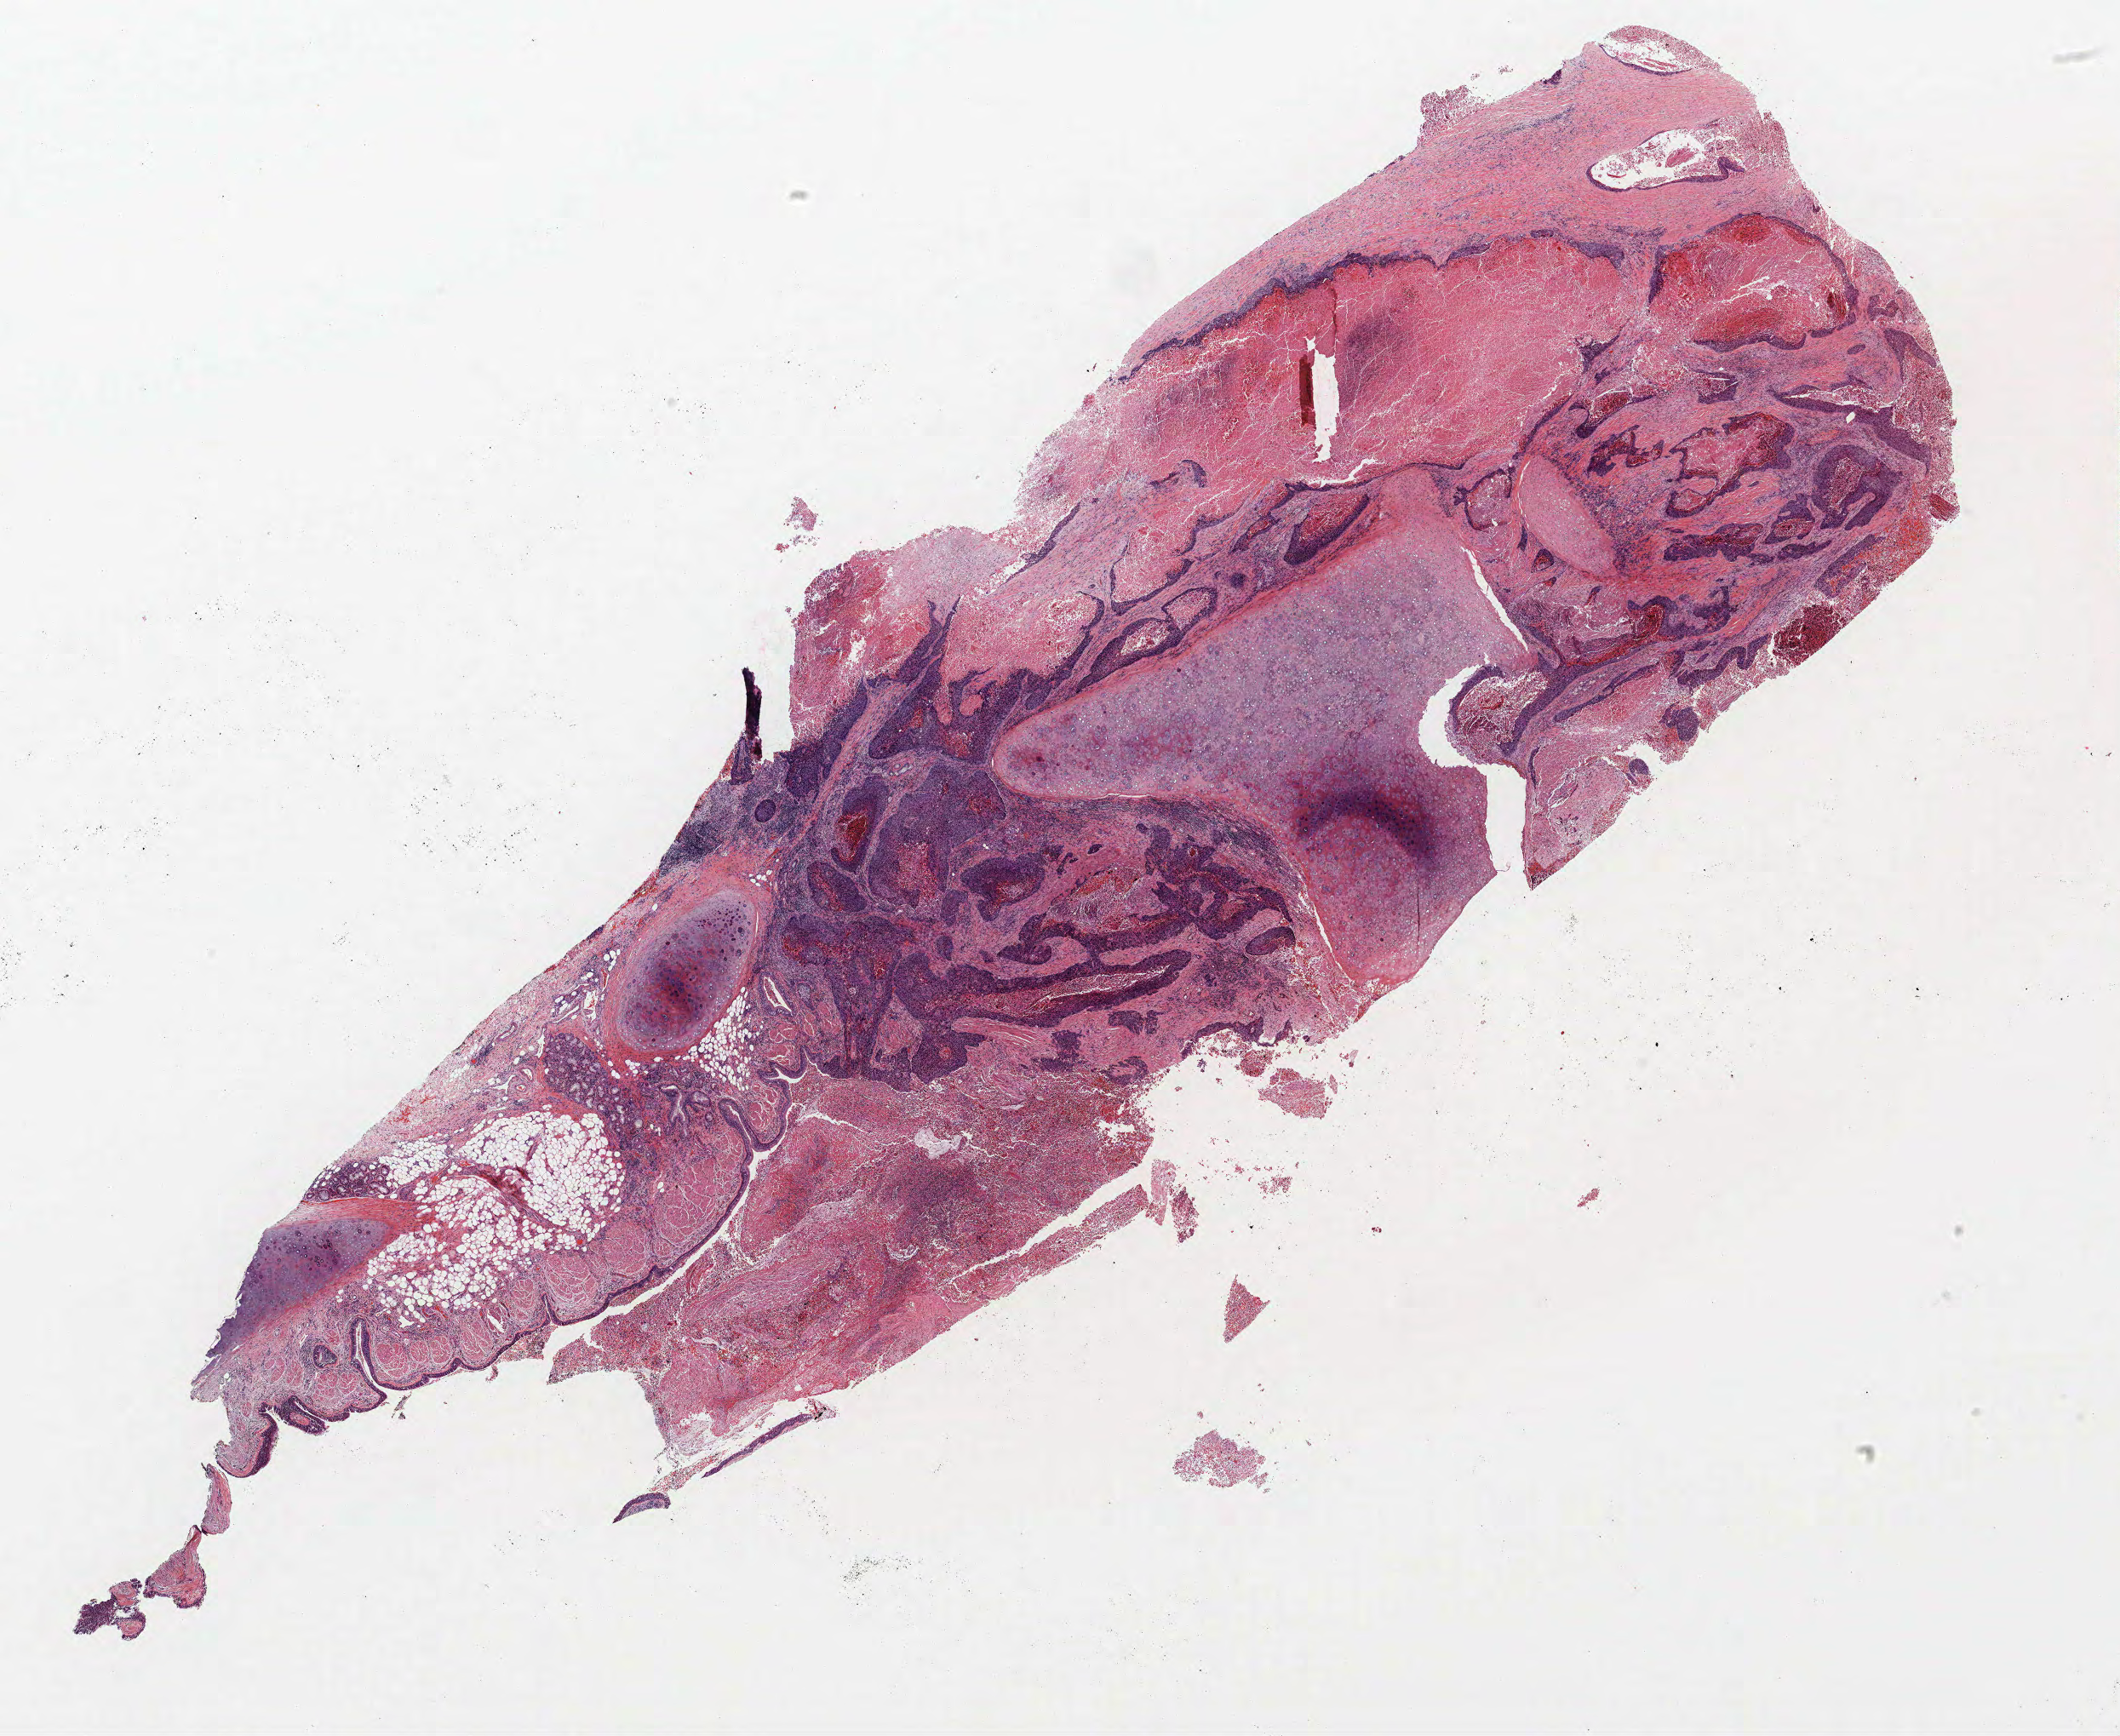
Whole-slide histology image, H&E-stained — shown as a low-resolution overview of the whole scanned area (about 19.9 x 16.3 mm); FFPE section; lung. Male, age 74 at enrolment. Current smoker at enrolment. Grade: poorly differentiated (G3).
- participant's lung-cancer diagnosis: Squamous cell carcinoma, NOS (ICD-O-3 8070/3)
- primary tumour location (clinical record): right lower lobe
- stage (AJCC 6th edition): IIB
- tumour size (pathology): 80 mm
- ICD-O-3 topography: lower lobe of lung (C34.3)